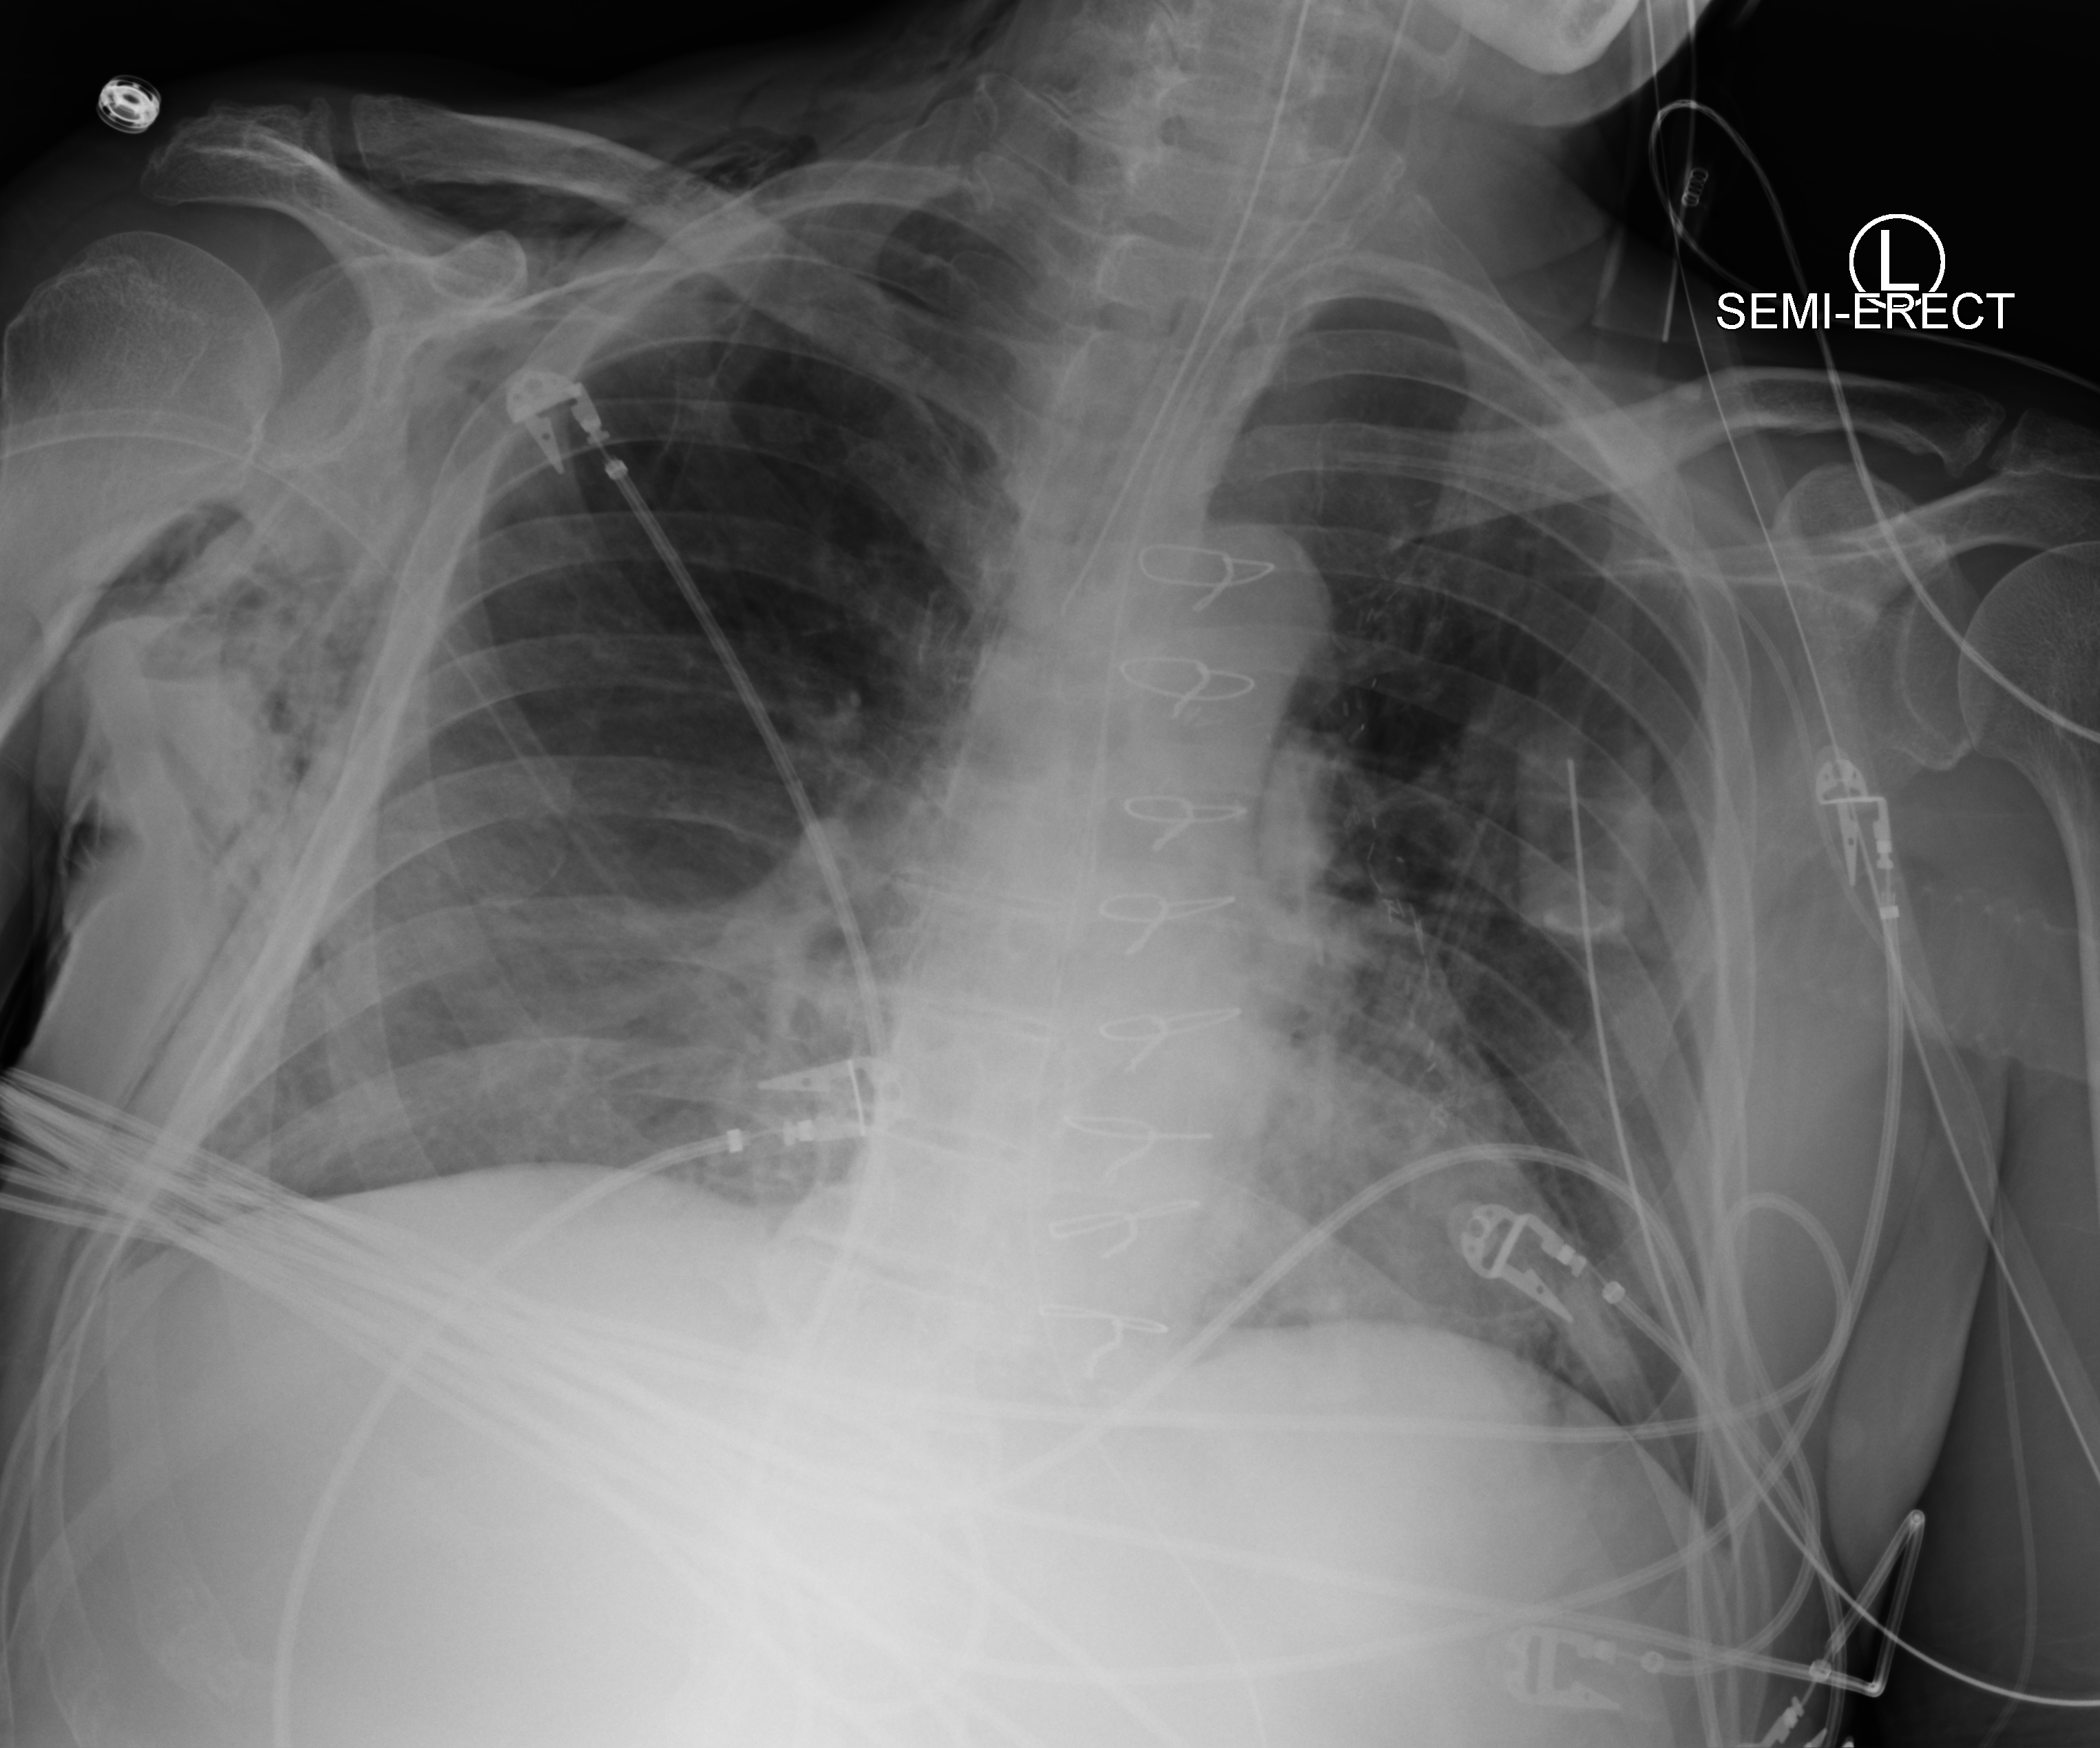
Portable chest radiograph; anteroposterior (AP) projection. Male patient hospitalised with COVID-19, age 60–74 years.
From the hospital-stay record, not from the radiograph (when in the stay this image was taken is not recorded):
- mechanically ventilated during this hospital stay: yes
- length of hospital stay: 22 days